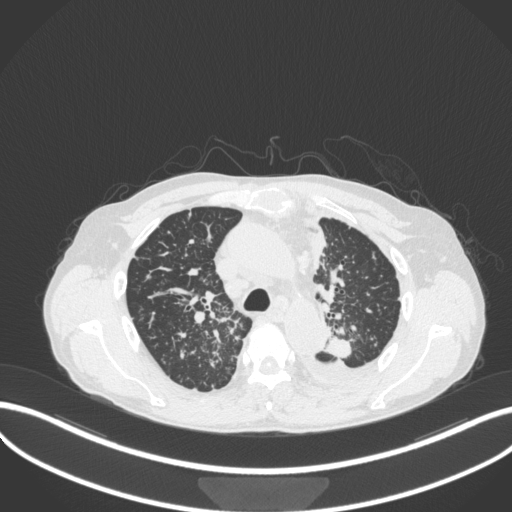
Chest CT, one axial slice. Position 254 of 319 along the scan axis. Reconstruction kernel B31f. Lung window (W 1500 / L -600 HU). 1 mm slice thickness. 512 × 512 image matrix. Male patient, age 58 years. Case-level facts recorded for this patient, not image findings: clinical TNM (as recorded): T1c N3 M1.
Structures marked on this image (rectangle marked by the reading radiologist):
- lung tumour (recorded histology: adenocarcinoma): bounding box [x1, y1, x2, y2] px = [322, 332, 355, 360]